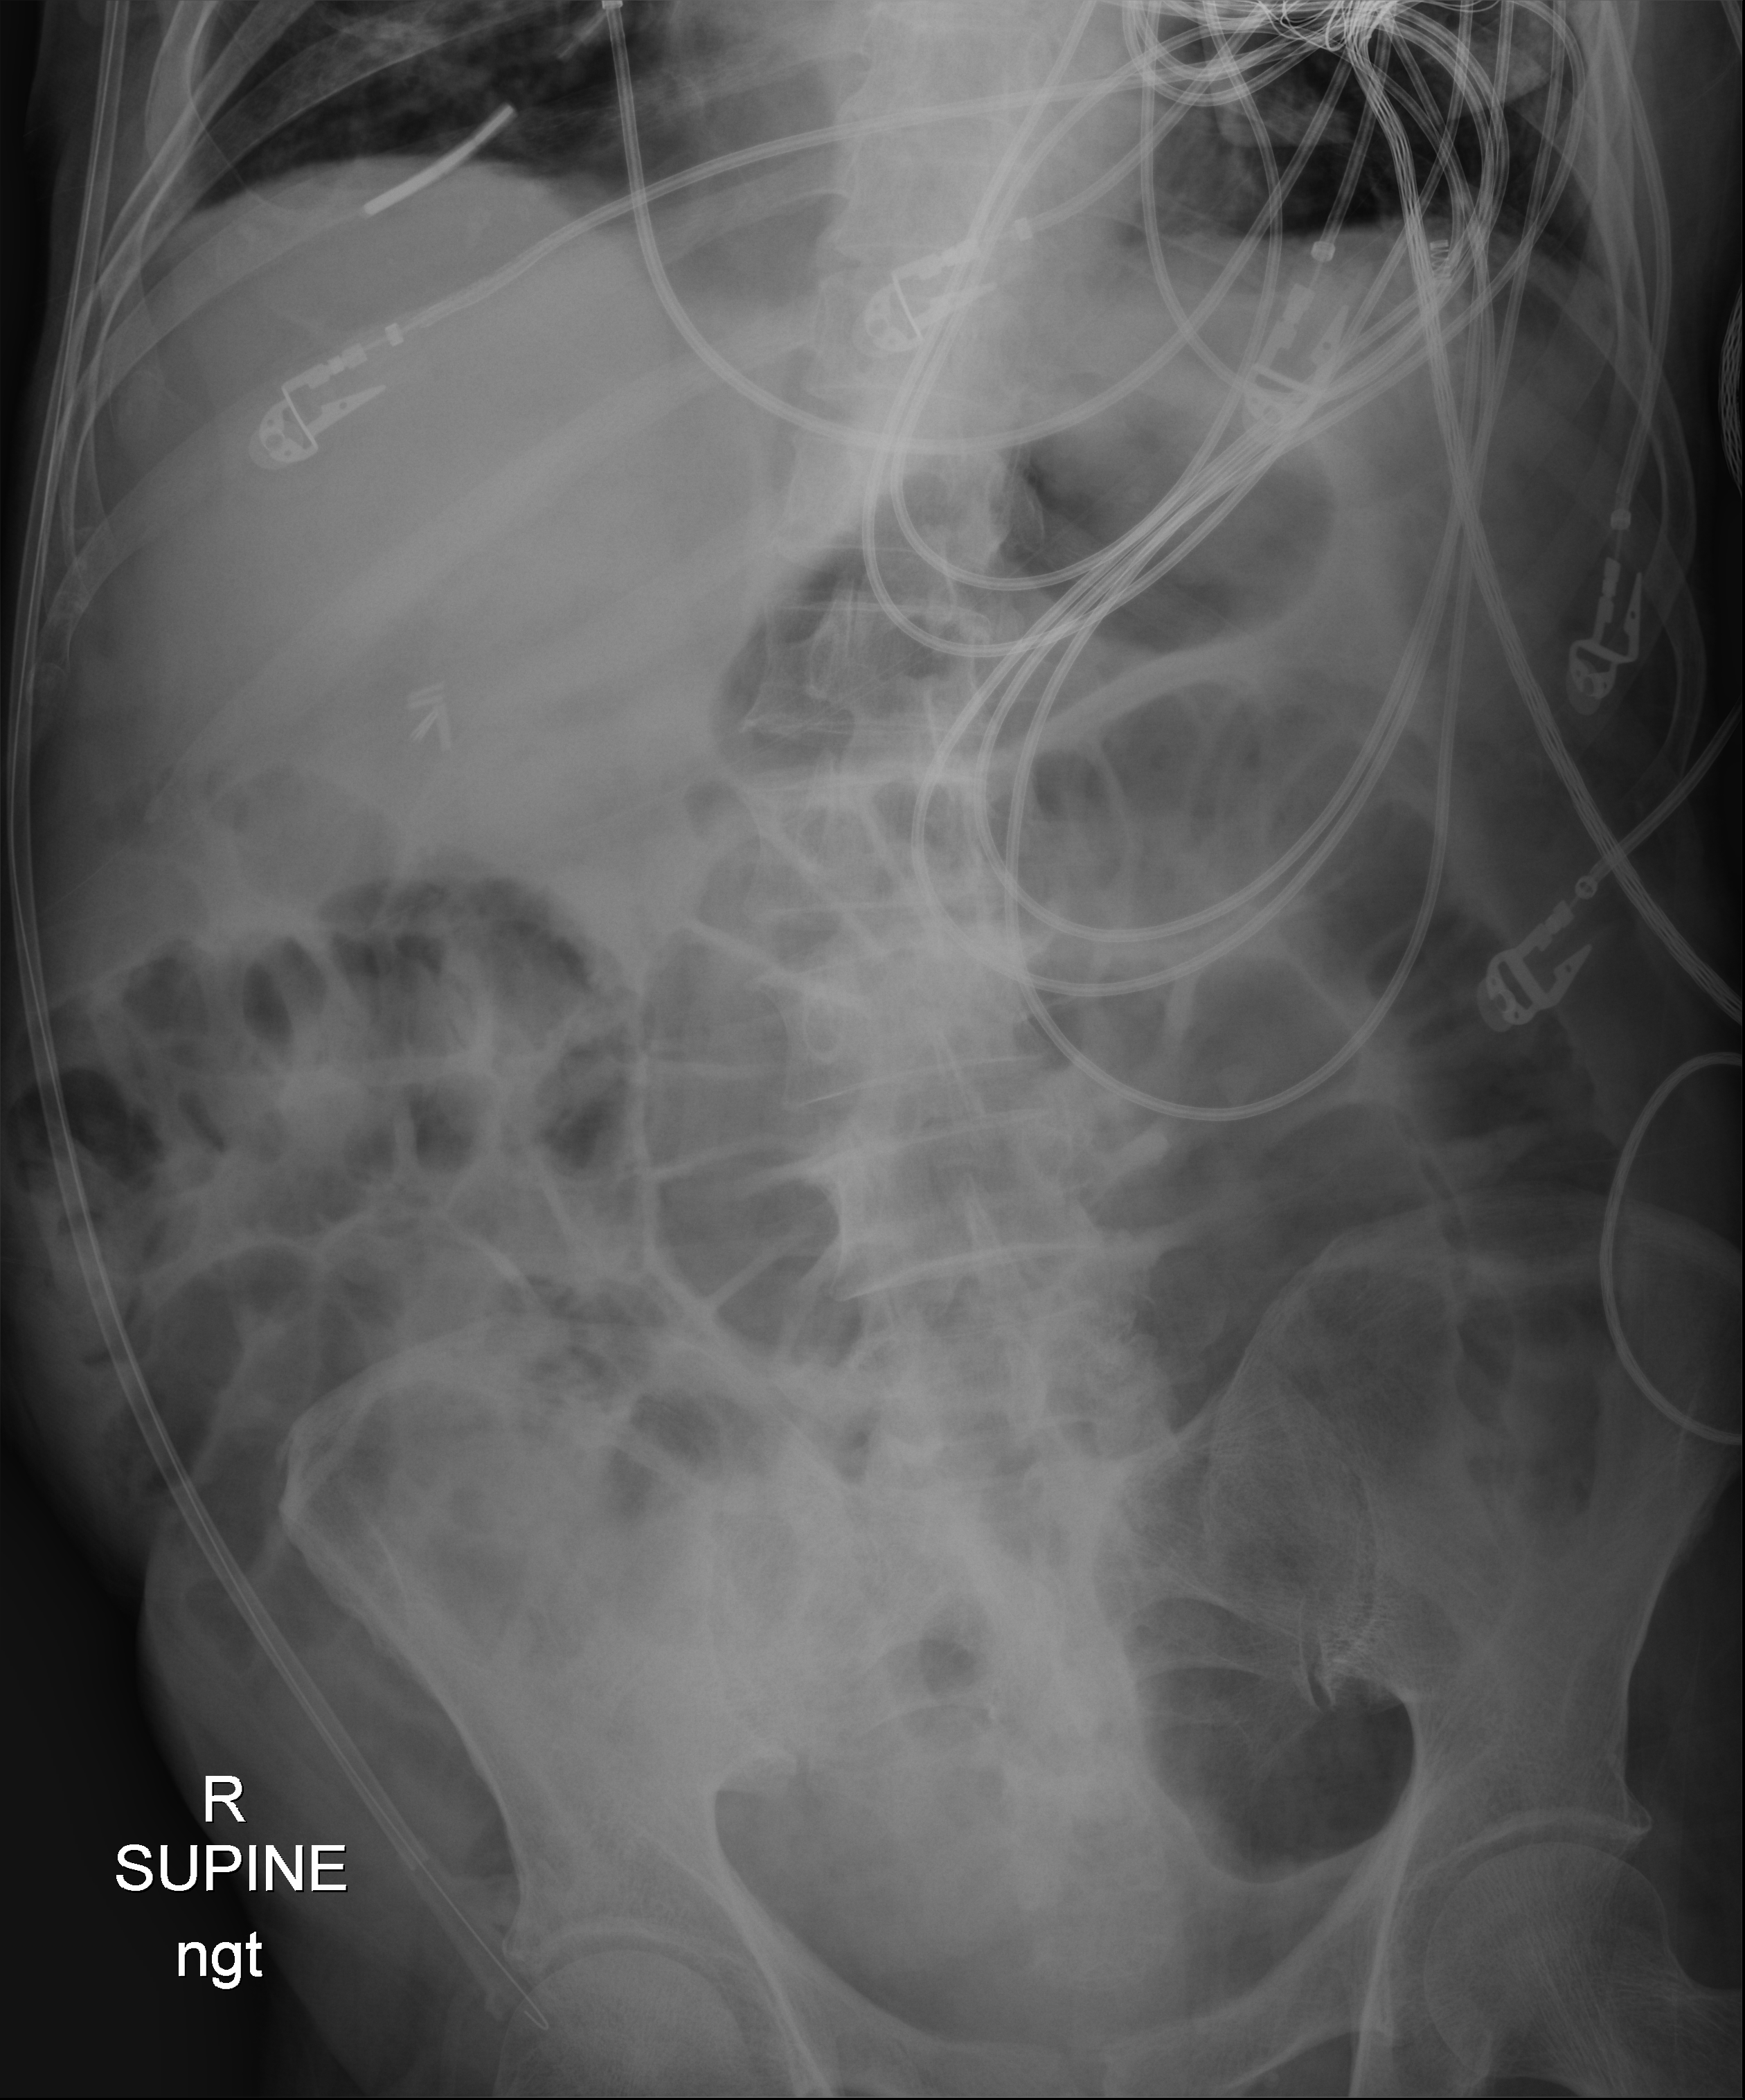
Abdomen X-ray (portable); anteroposterior (AP) projection. Male patient hospitalised with COVID-19, age 75–90 years.
Hospital-stay facts (about this admission, not read from this image; timing relative to this image not recorded): length of hospital stay: 70 days; admitted to intensive care during this hospital stay: yes.